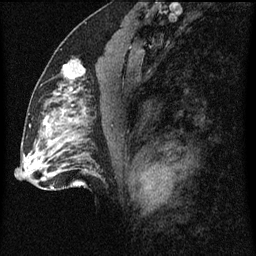
Breast MRI (dynamic contrast-enhanced), one sagittal slice. Slice 38 of 60 in the series (ordered by position). Dynamic contrast-enhanced series, image 2 of 3 at this slice position (ordered by acquisition). 1.5 T. TE 4.2 ms, TR 8 ms. 2 mm slice thickness. 256 × 256 image matrix, field of view 180 × 180 mm. Patient: female, 51 years.
Structures marked on this image (semi-automatically segmented with operator editing):
- analysis volume of interest (the breast-tissue region the enhancement analysis was run in; not a lesion): bounding box <54,50,91,103> (left, top, right, bottom; pixels)
- tumour enhancement mask (voxels above the 70 % enhancement threshold inside the analysis volume of interest): <55,88,78,95>